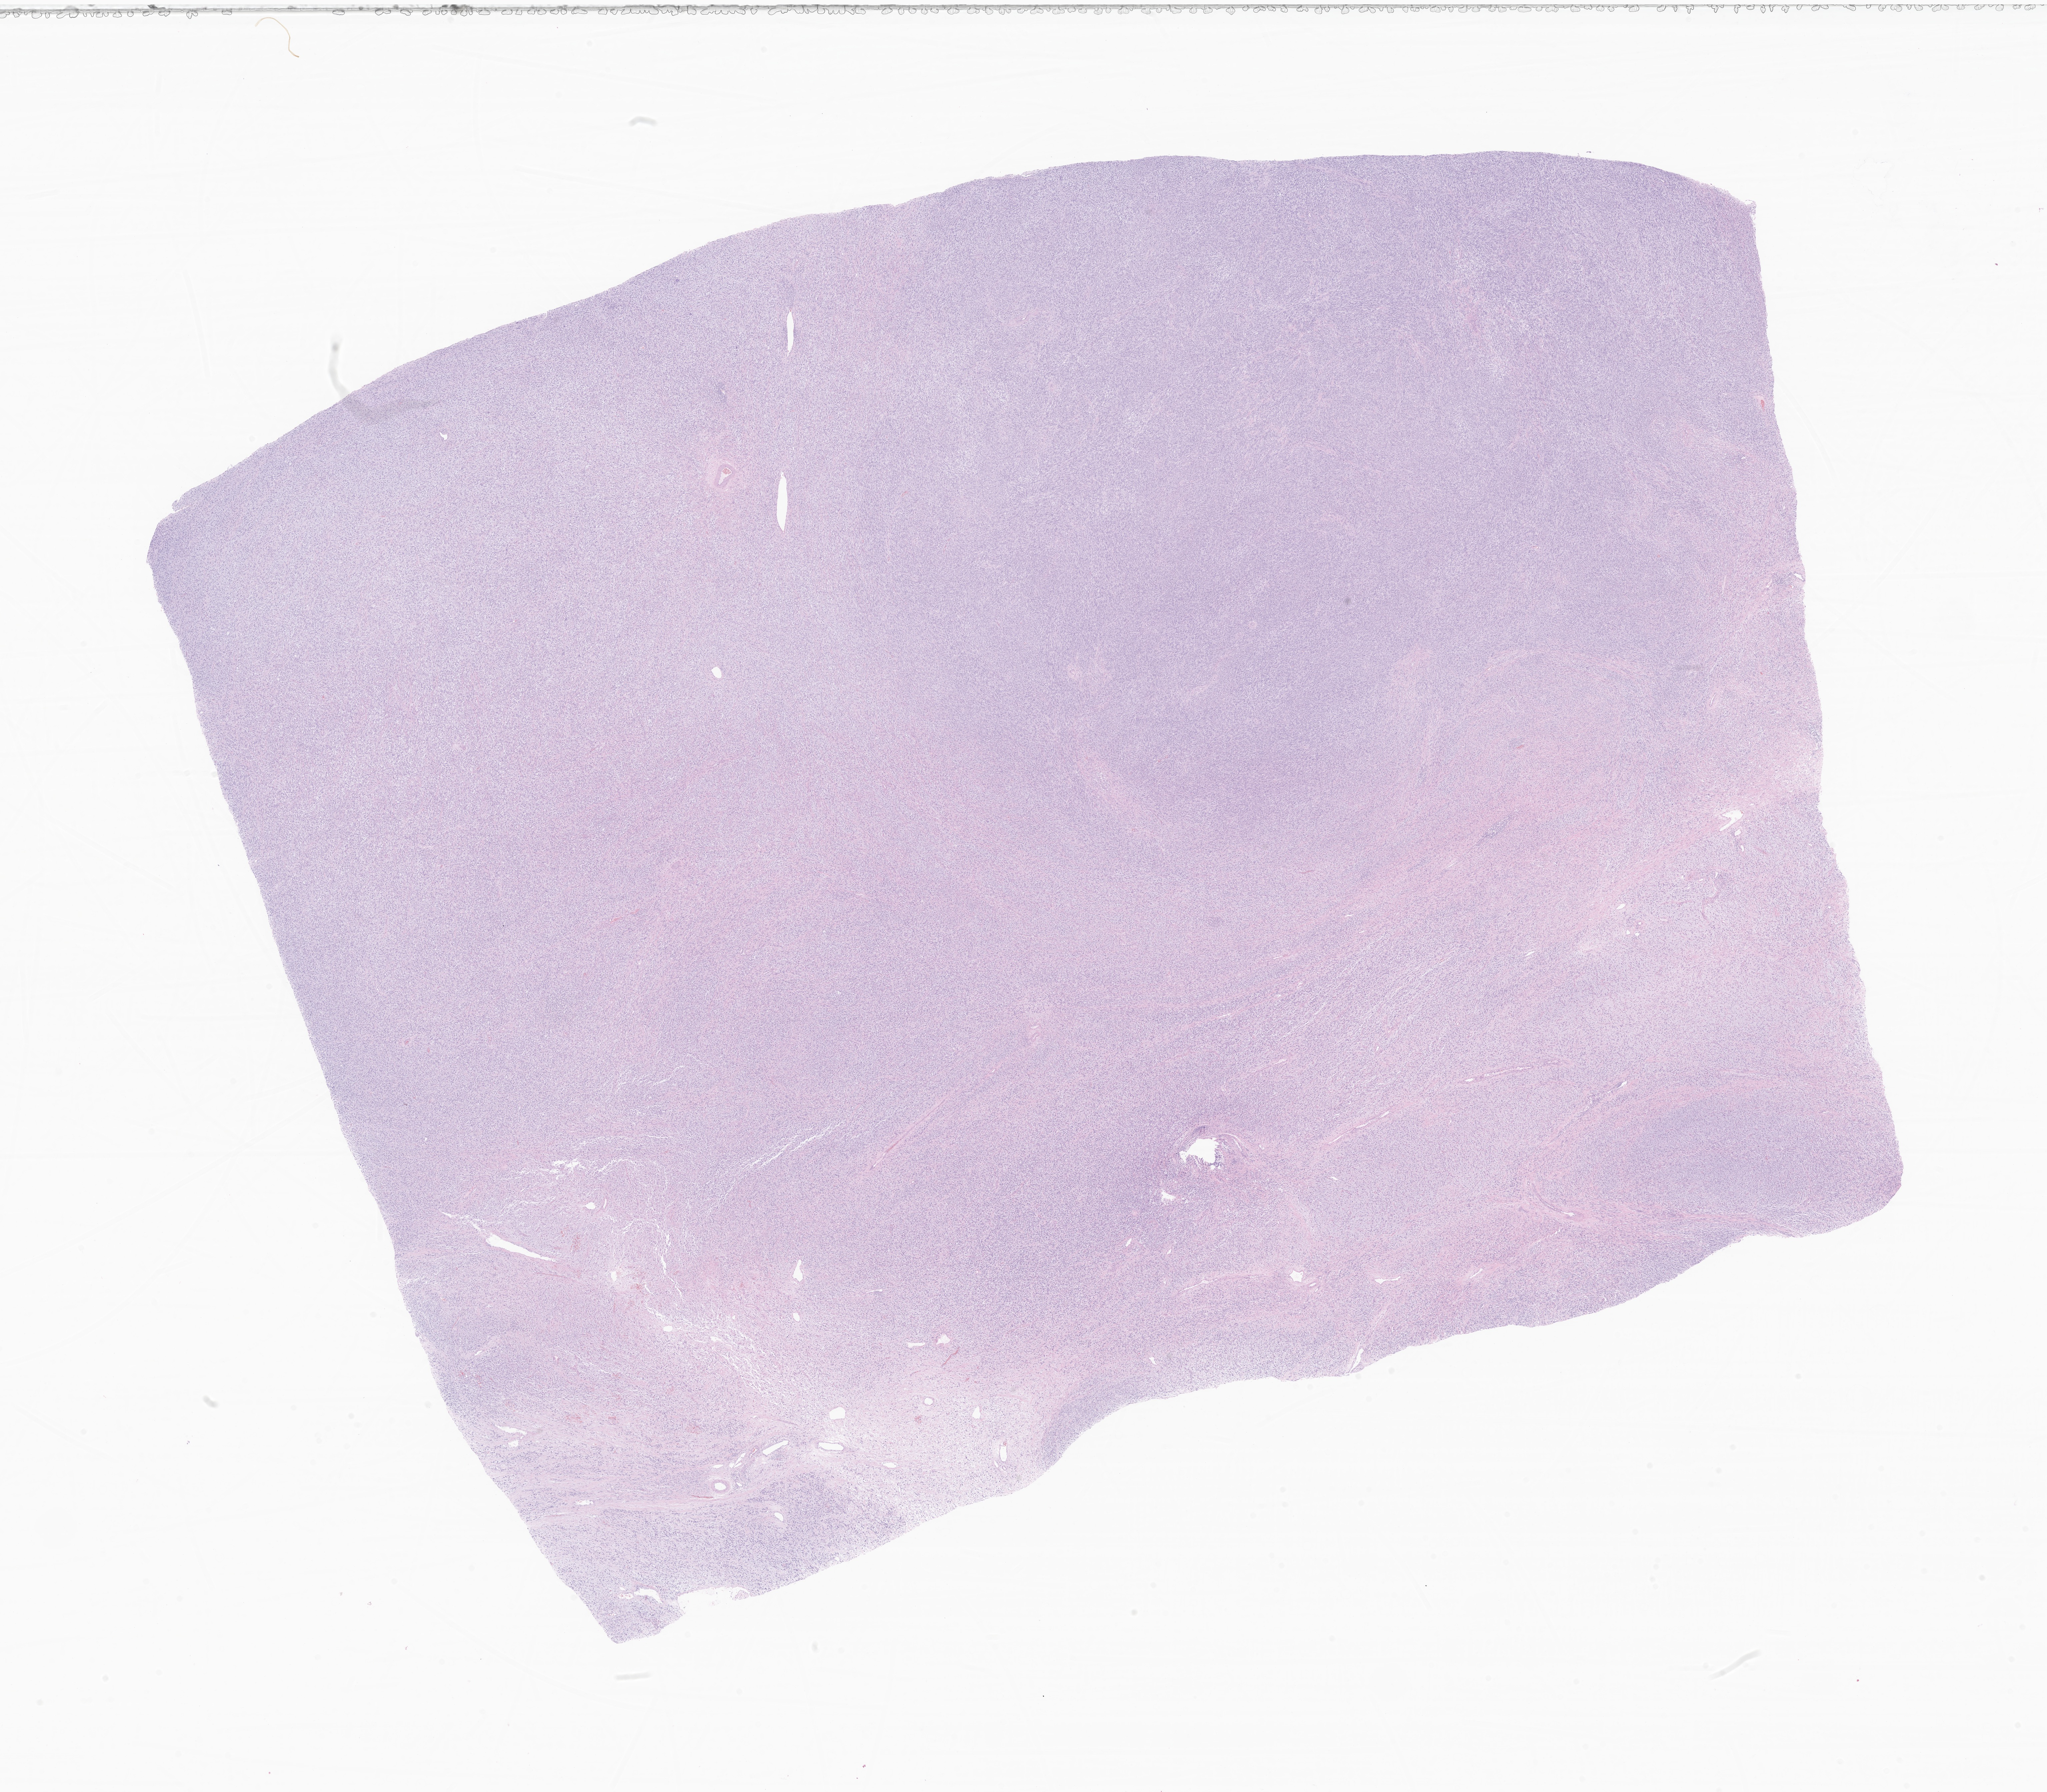
Haematoxylin and eosin whole-slide image of tumor tissue from the testis — a low-resolution overview of the entire scanned area, about 25.9 x 22.7 mm; FFPE section. Patient male; age 166 months (13 years 10 months).
Recorded diagnosis: Spindle cell rhabdomyosarcoma.